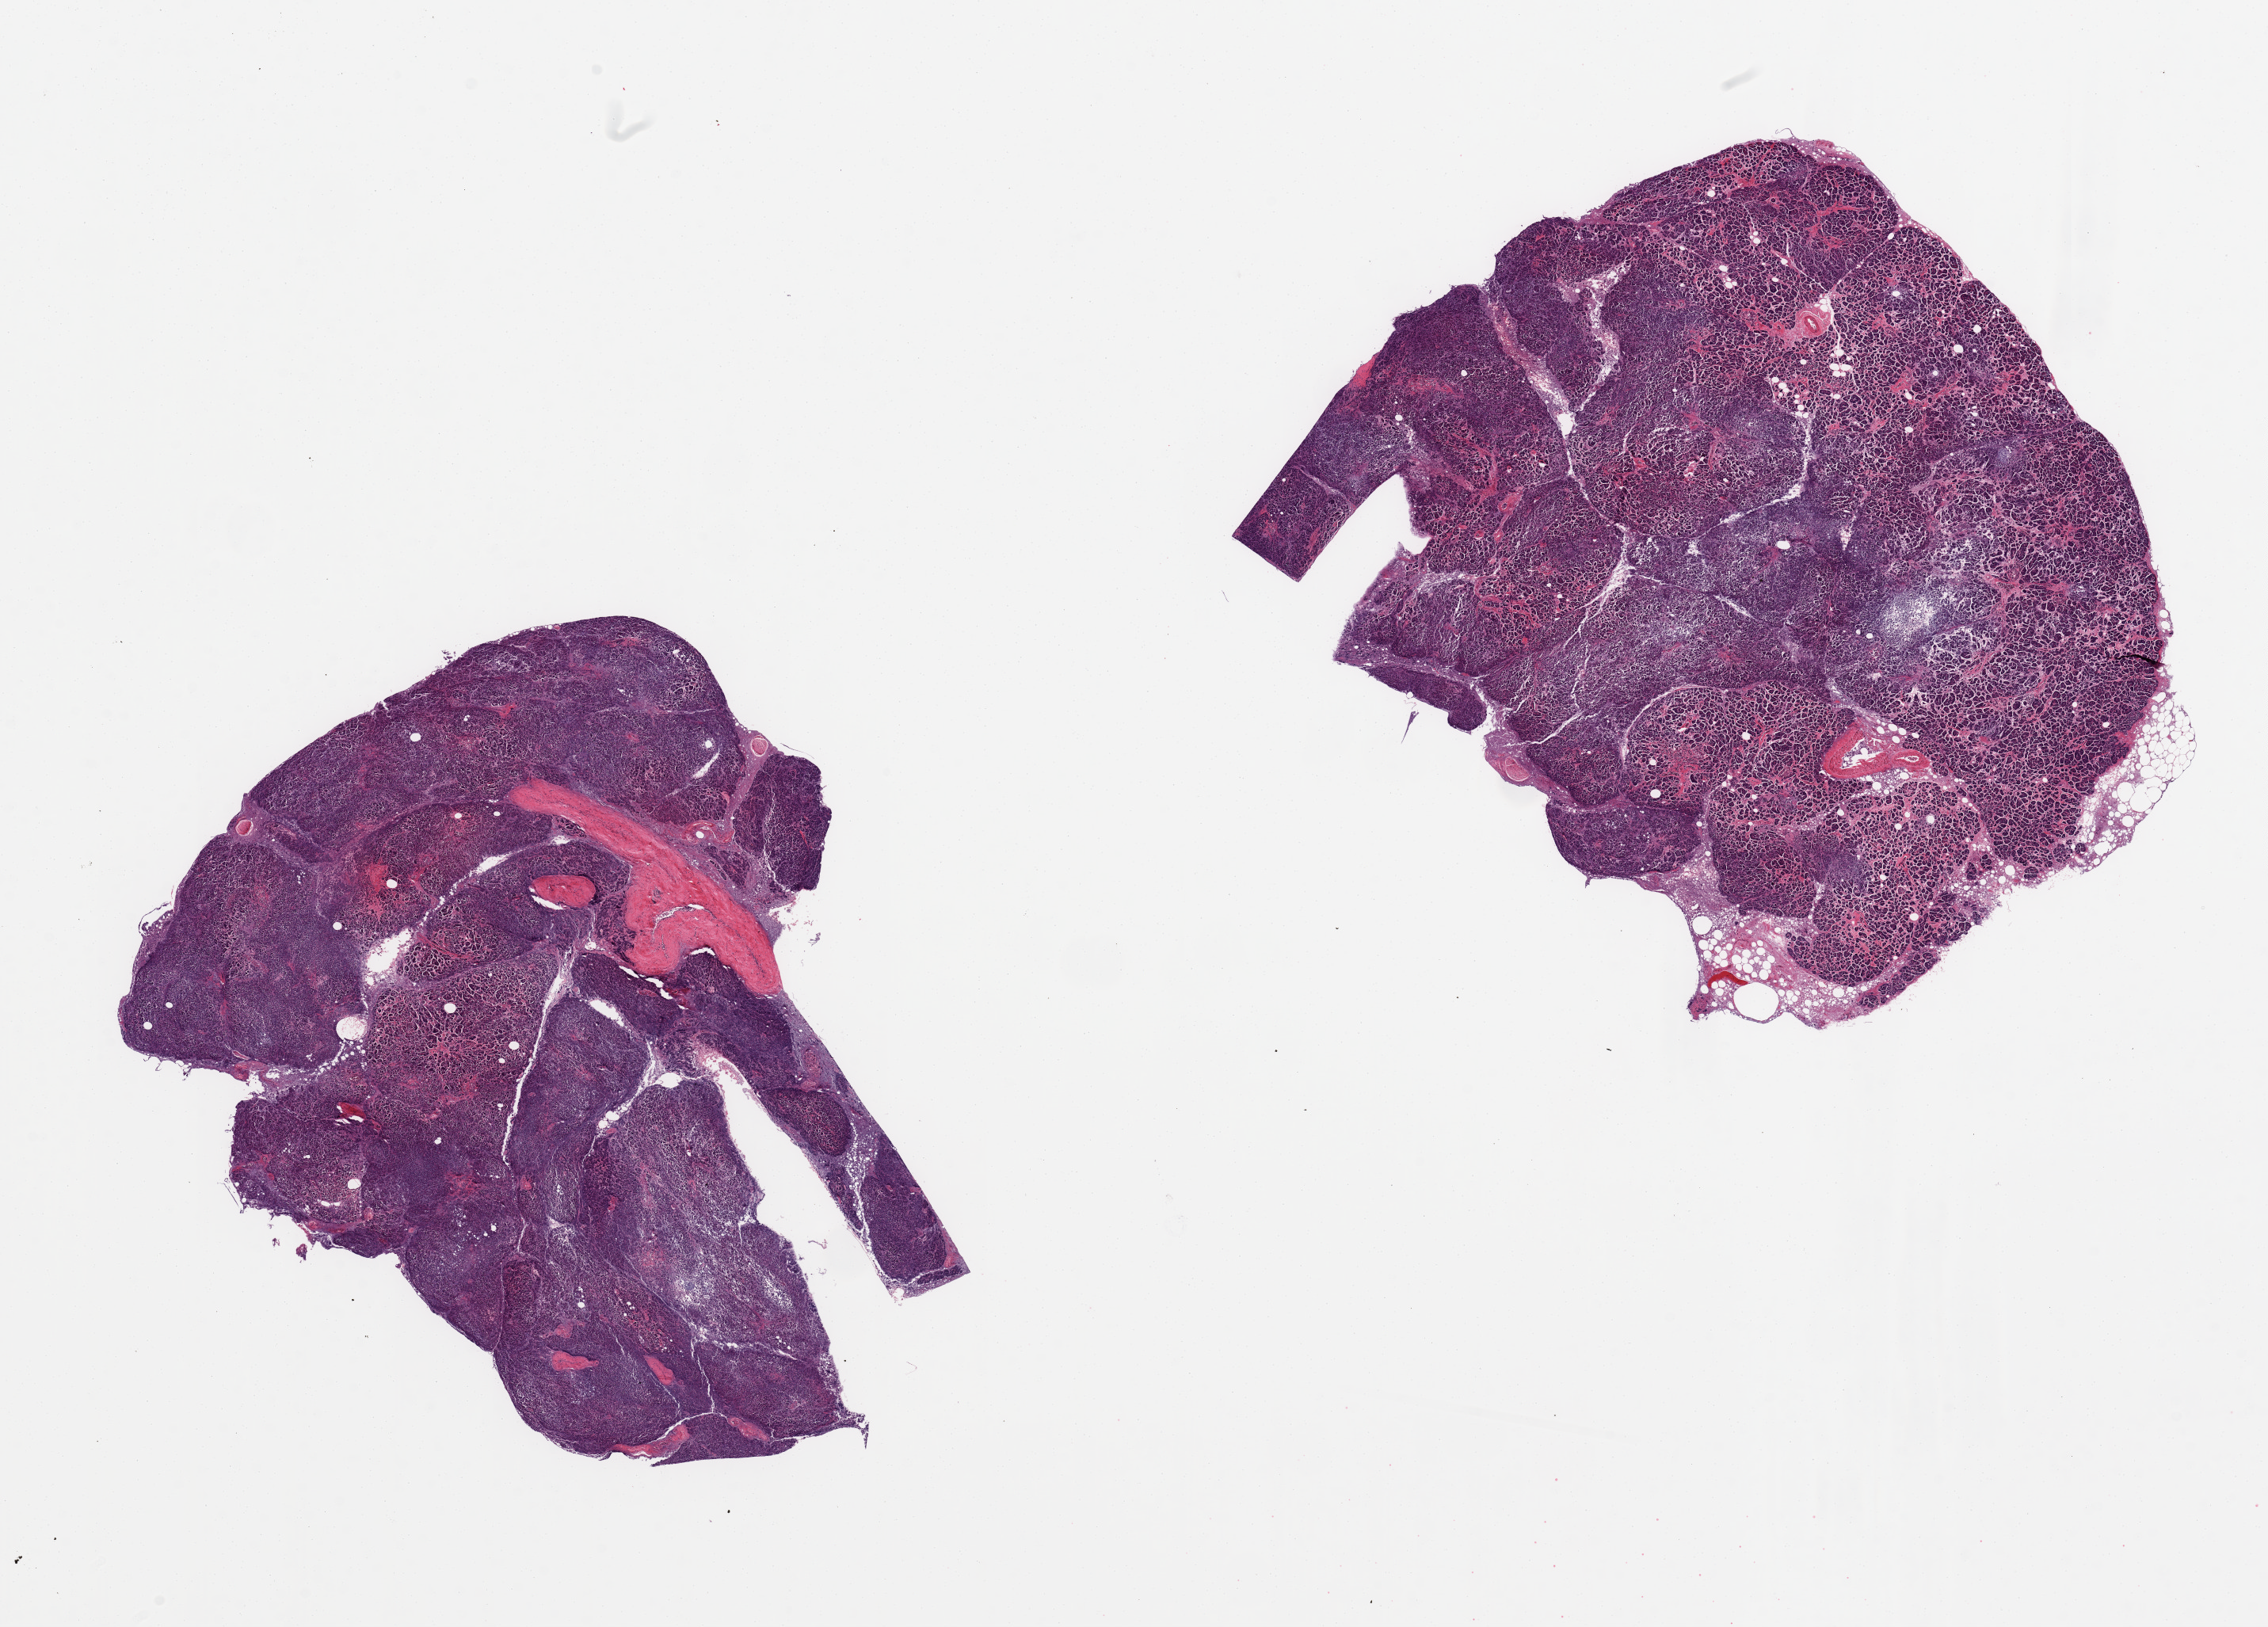
Whole-slide image, H&E stain, brightfield, a low-resolution overview of the entire scanned area, about 22.6 x 16.2 mm; PAXgene-fixed paraffin-embedded (PFPE) section; sampled site (target tissue): pancreas; tissue donor sample. Female donor.
Review note (as recorded): 2 pieces; moderate to severe autolysis.